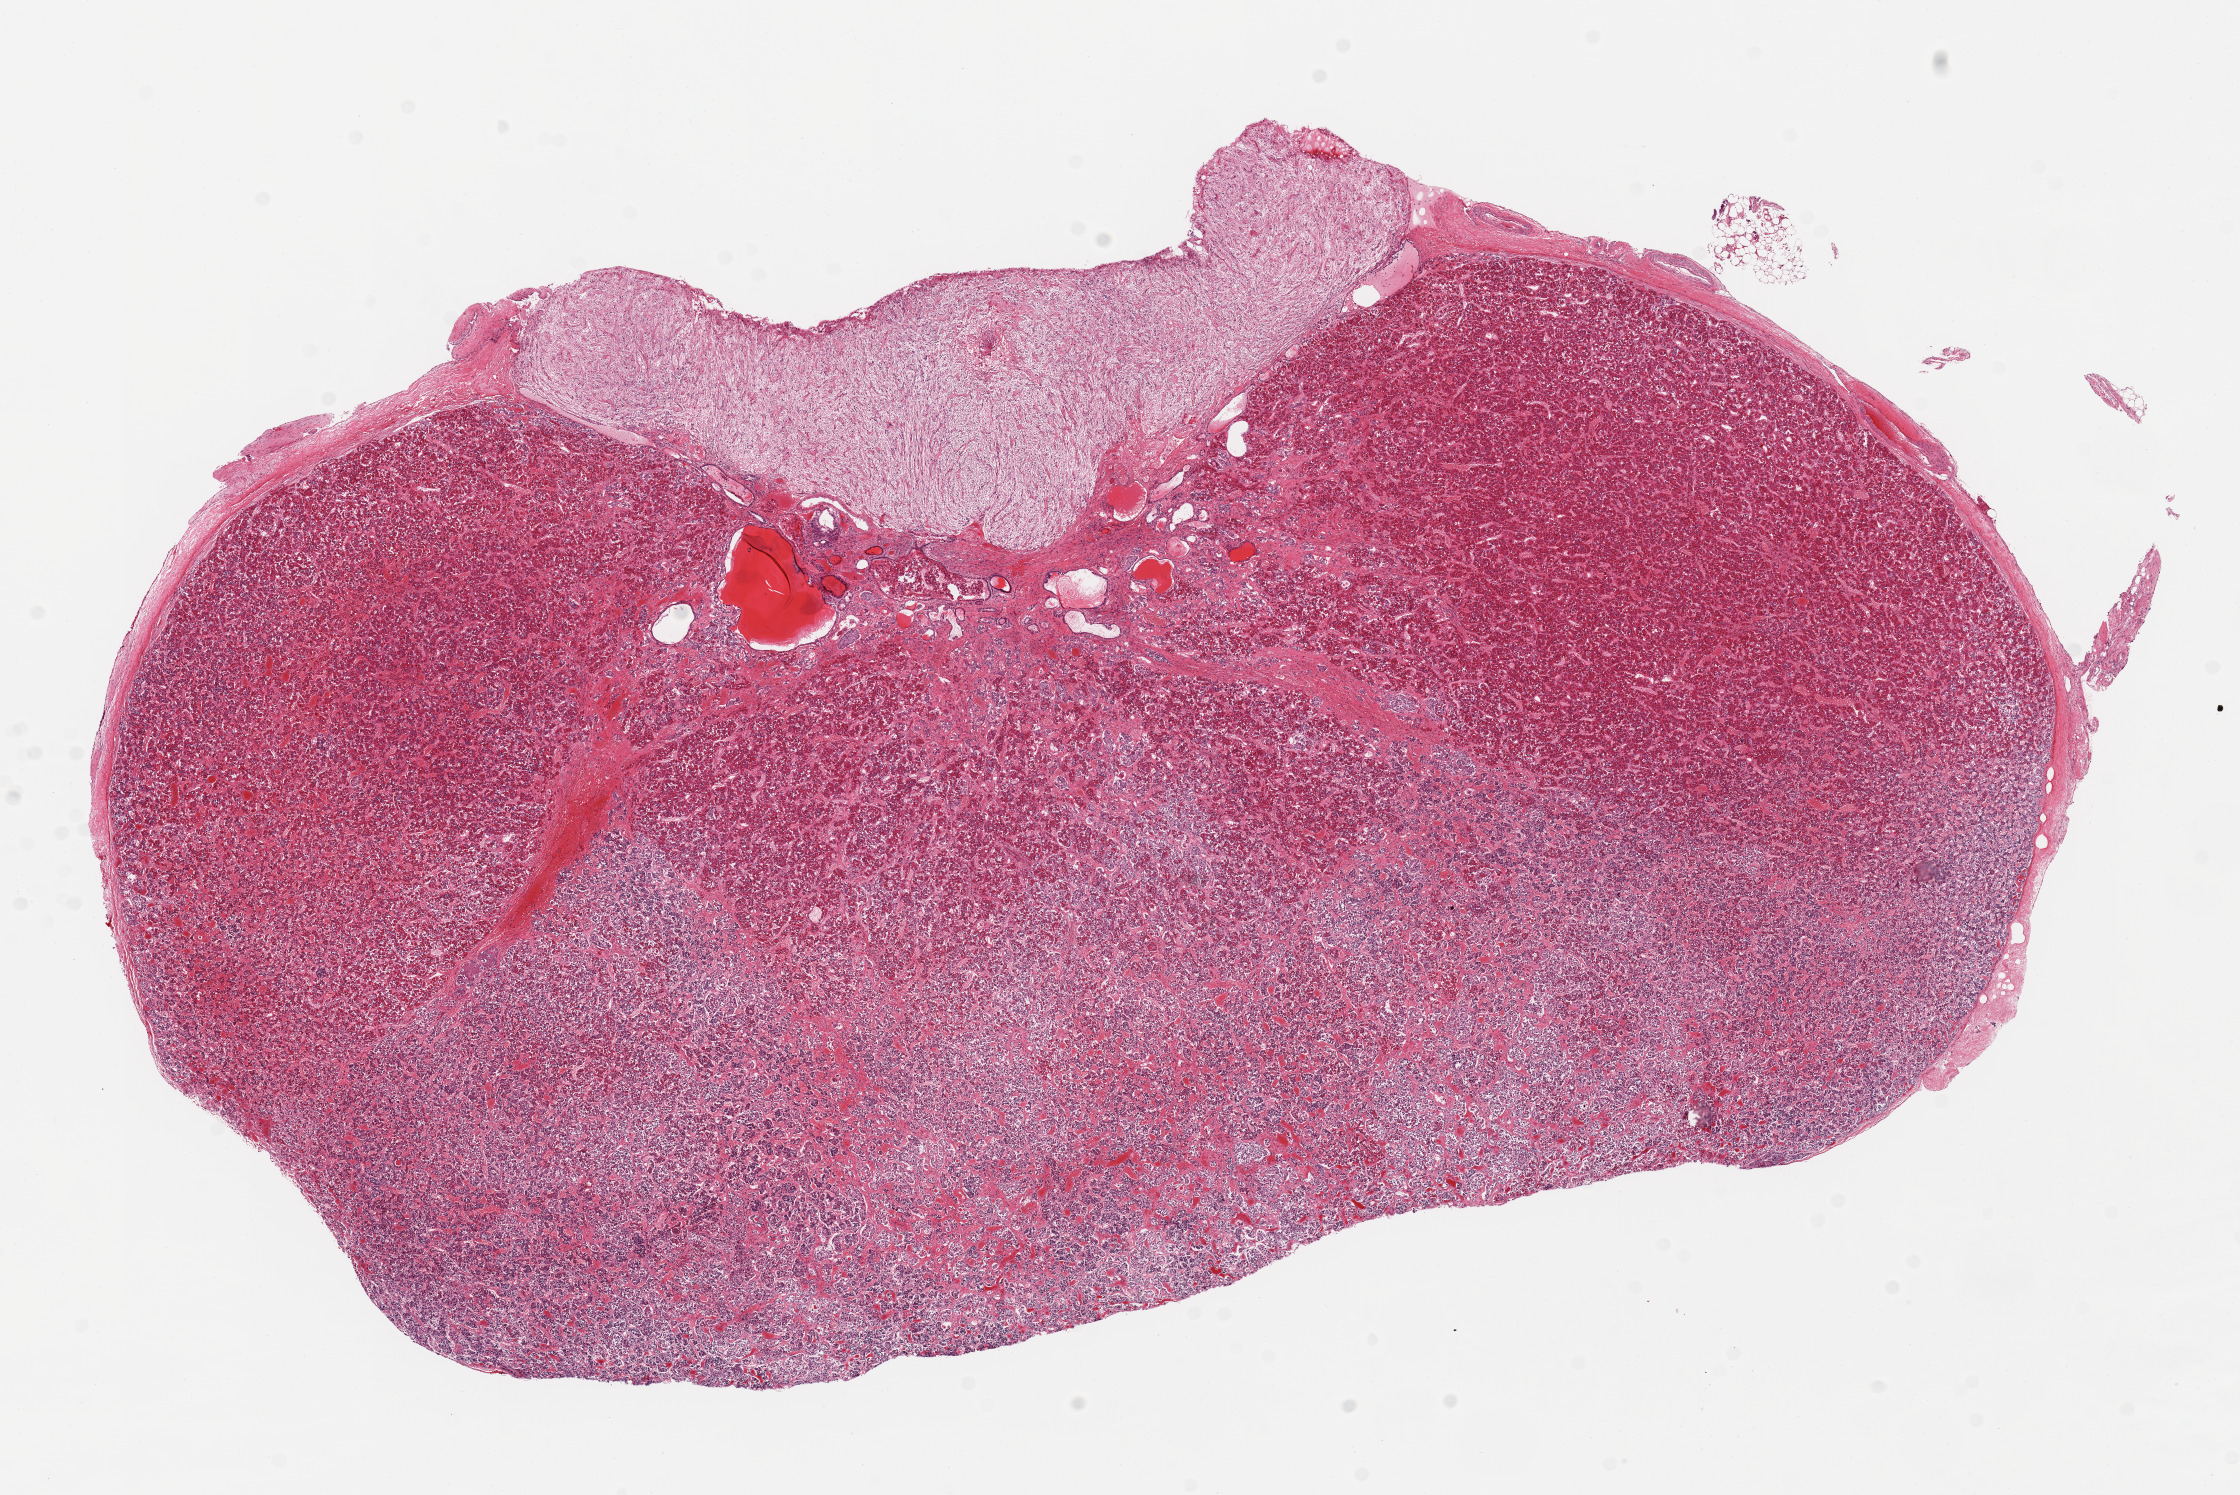
Digitized haematoxylin and eosin-stained section, brightfield — low-resolution overview of the scanned area, about 17.7 x 11.8 mm. PAXgene-fixed paraffin-embedded (PFPE) section. Target tissue: pituitary. Donor tissue sample. Donor sex: male.
Reviewer comment on this tissue sample: 1 pieces; adenohypophysis, neurohypophysis, and pars intermedia with some cystically dilated spaces.